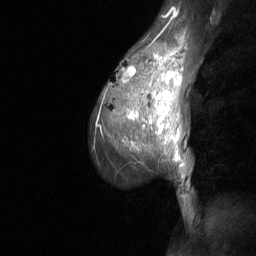
Breast MRI (dynamic contrast-enhanced), one sagittal slice. Position 47 of 64 along the scan axis. Dynamic contrast-enhanced study with each time point stored as its own series, time point 2 of 3 at this slice position (early post-contrast, ordered by acquisition time). 1.5 T. TE 4.8 ms, TR 27 ms. 2 mm slice thickness. 256 × 256 image matrix, field of view 200 × 200 mm. Female patient, age 36 years. Case-level facts recorded for this patient, not image findings: setting: breast cancer imaged before/during neoadjuvant chemotherapy; receptor status: HR-positive, HER2-negative.
Annotated regions visible in this slice (semi-automatically segmented with operator editing):
- analysis volume of interest (the breast-tissue region the enhancement analysis was run in; not a lesion): bounding box (x1, y1, x2, y2) in pixels: (92, 45, 187, 210)
- tumour enhancement mask (voxels above the 90 % enhancement threshold inside the analysis volume of interest): (125, 46, 185, 142)